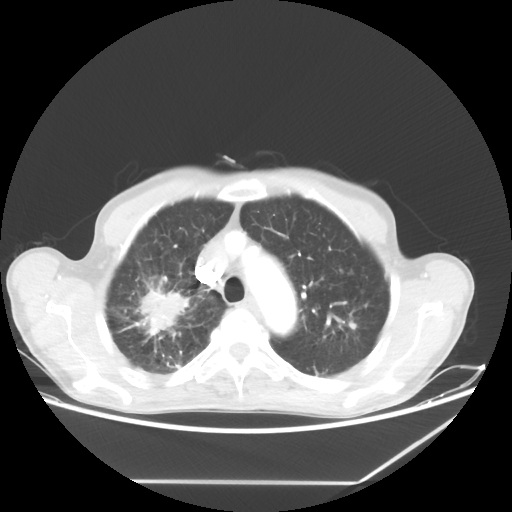
Chest CT, one axial slice. Slice 49 of 65 in the series (ordered by position). 80 kVp. Lung window (W 1500 / L -600 HU). 512 × 512 image matrix. Patient: male, 68 years. From the clinical record (not read from this slice): clinical TNM (as recorded): T3 N3 M0.
Annotated regions visible in this slice (rectangle marked by the reading radiologist):
- lung tumour (recorded histology: adenocarcinoma): box from (x=128, y=274) to (x=202, y=353) px